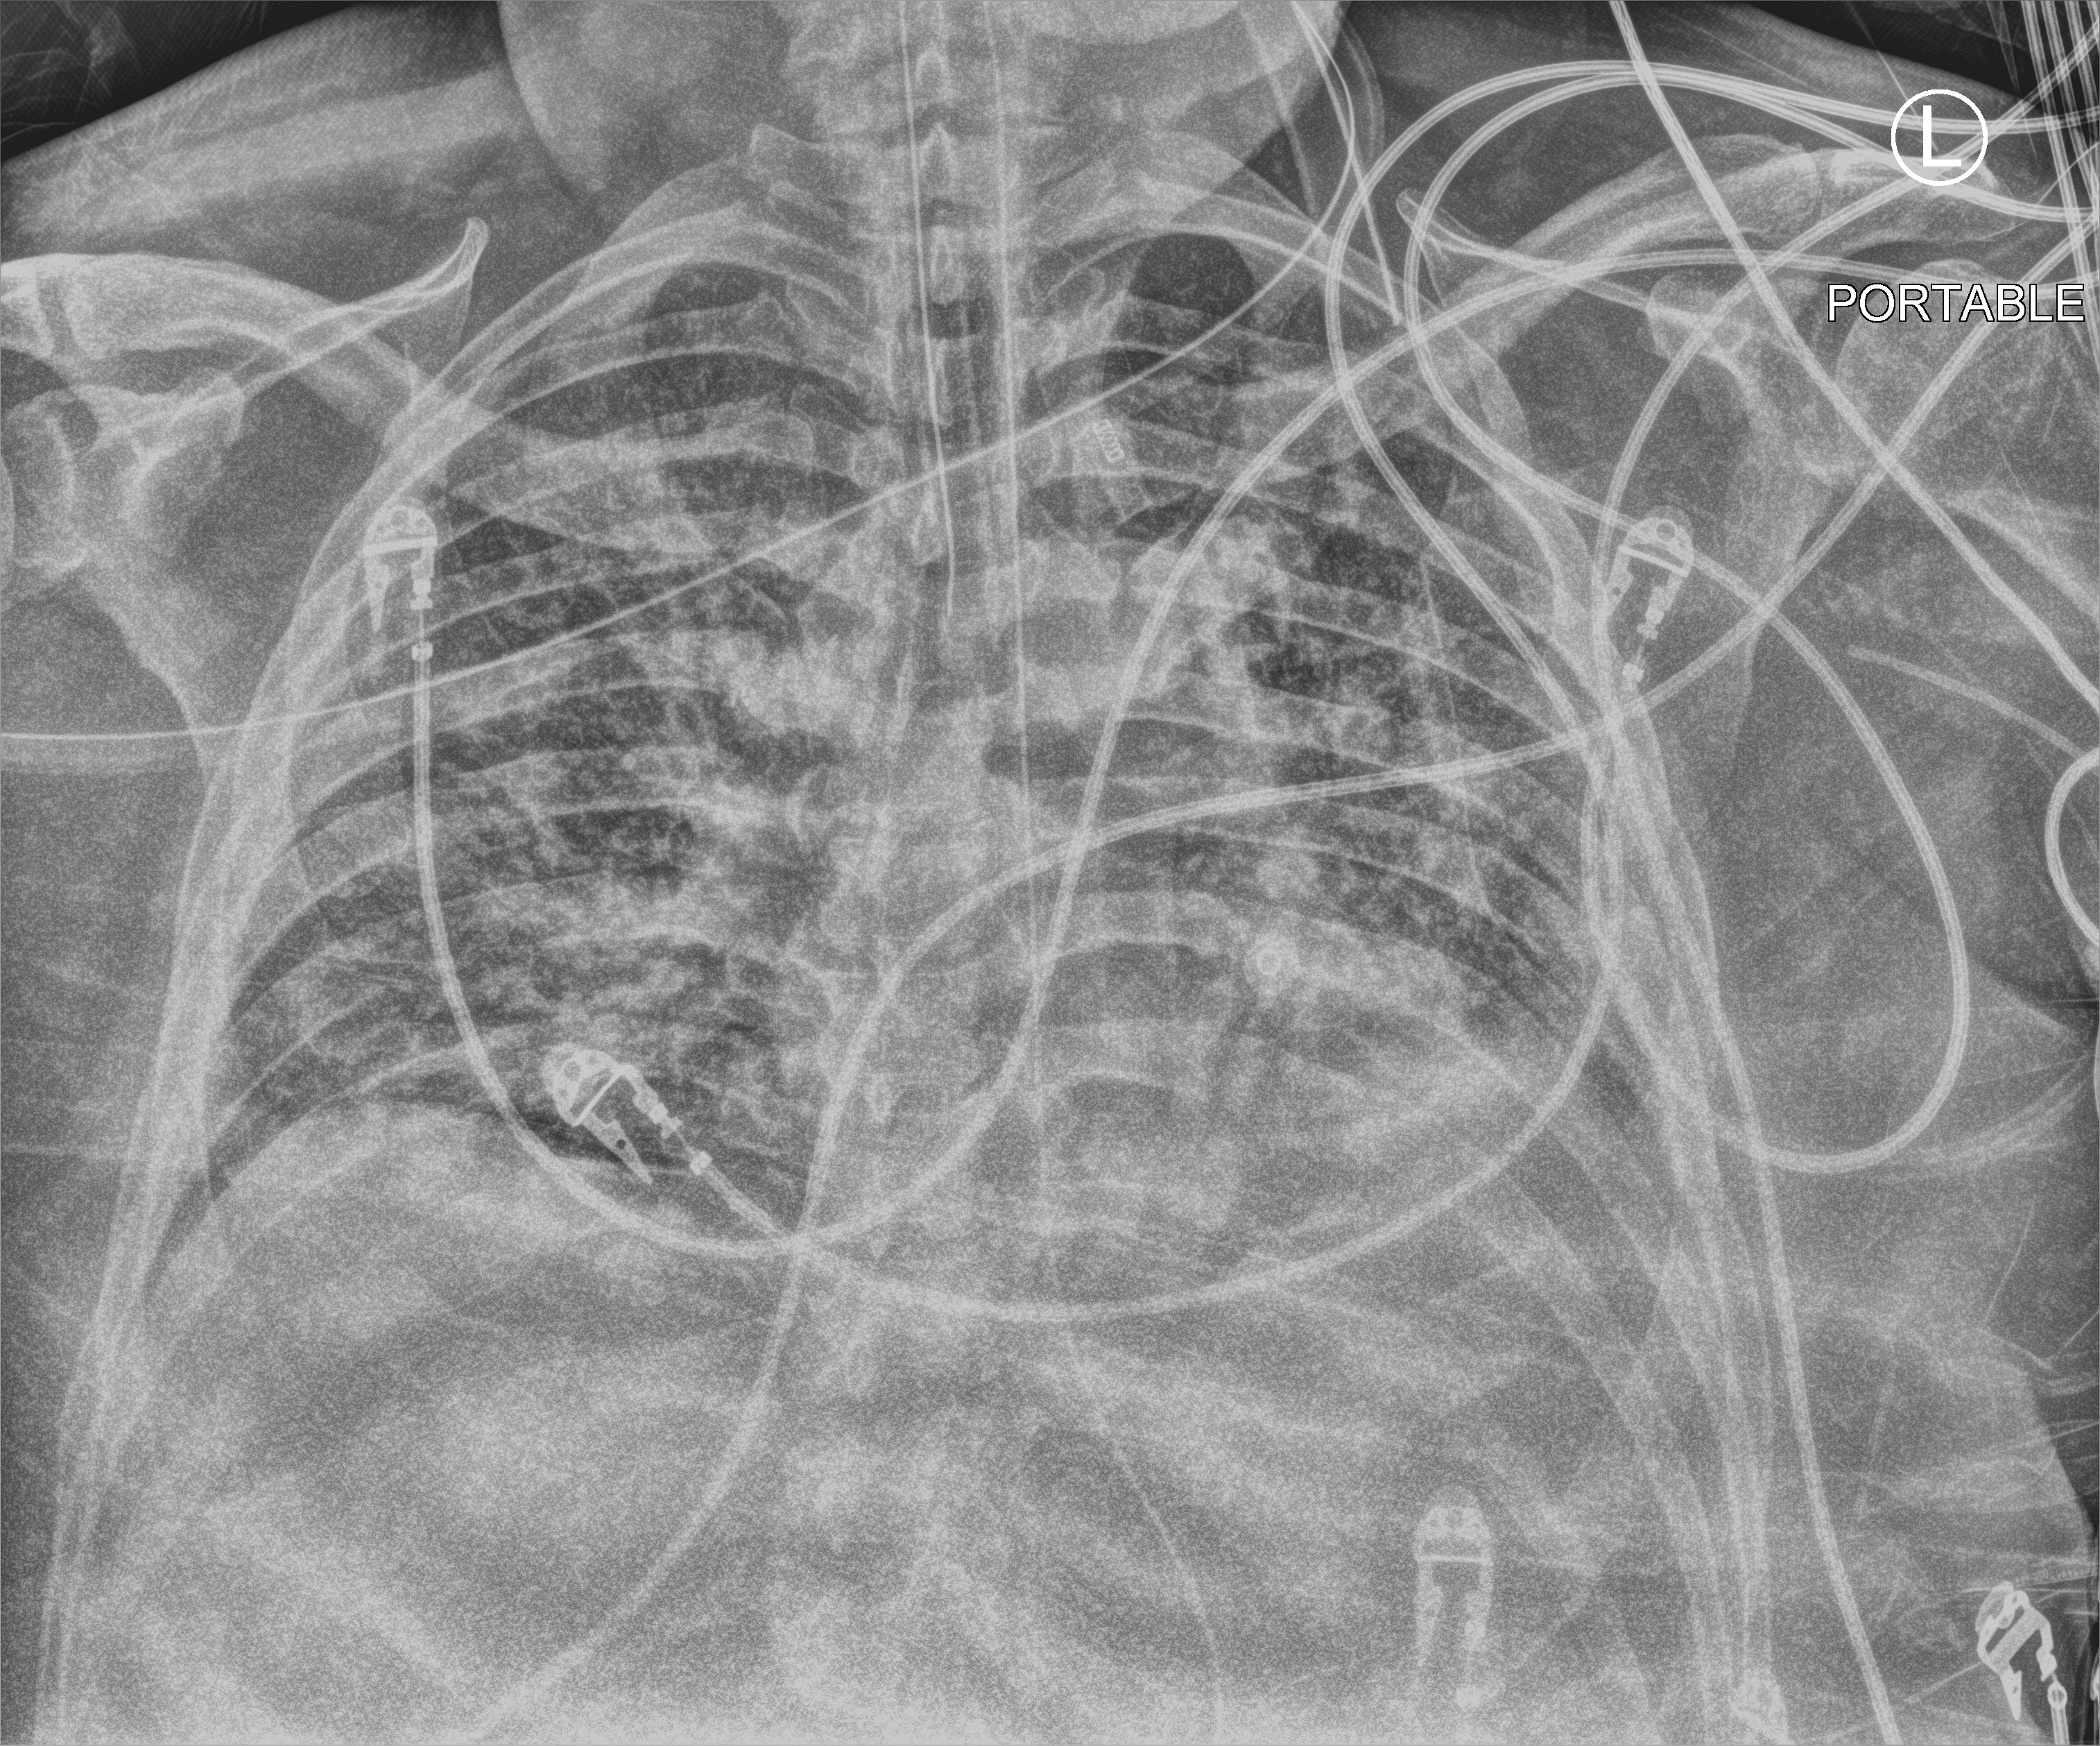
Bedside chest radiograph (computed radiography), anteroposterior (AP) projection. Patient hospitalised with COVID-19; male, aged 18–59 years.
Admission-level facts for this patient (not findings on this image; timing relative to this image not recorded): chronic kidney disease (admission record): no.